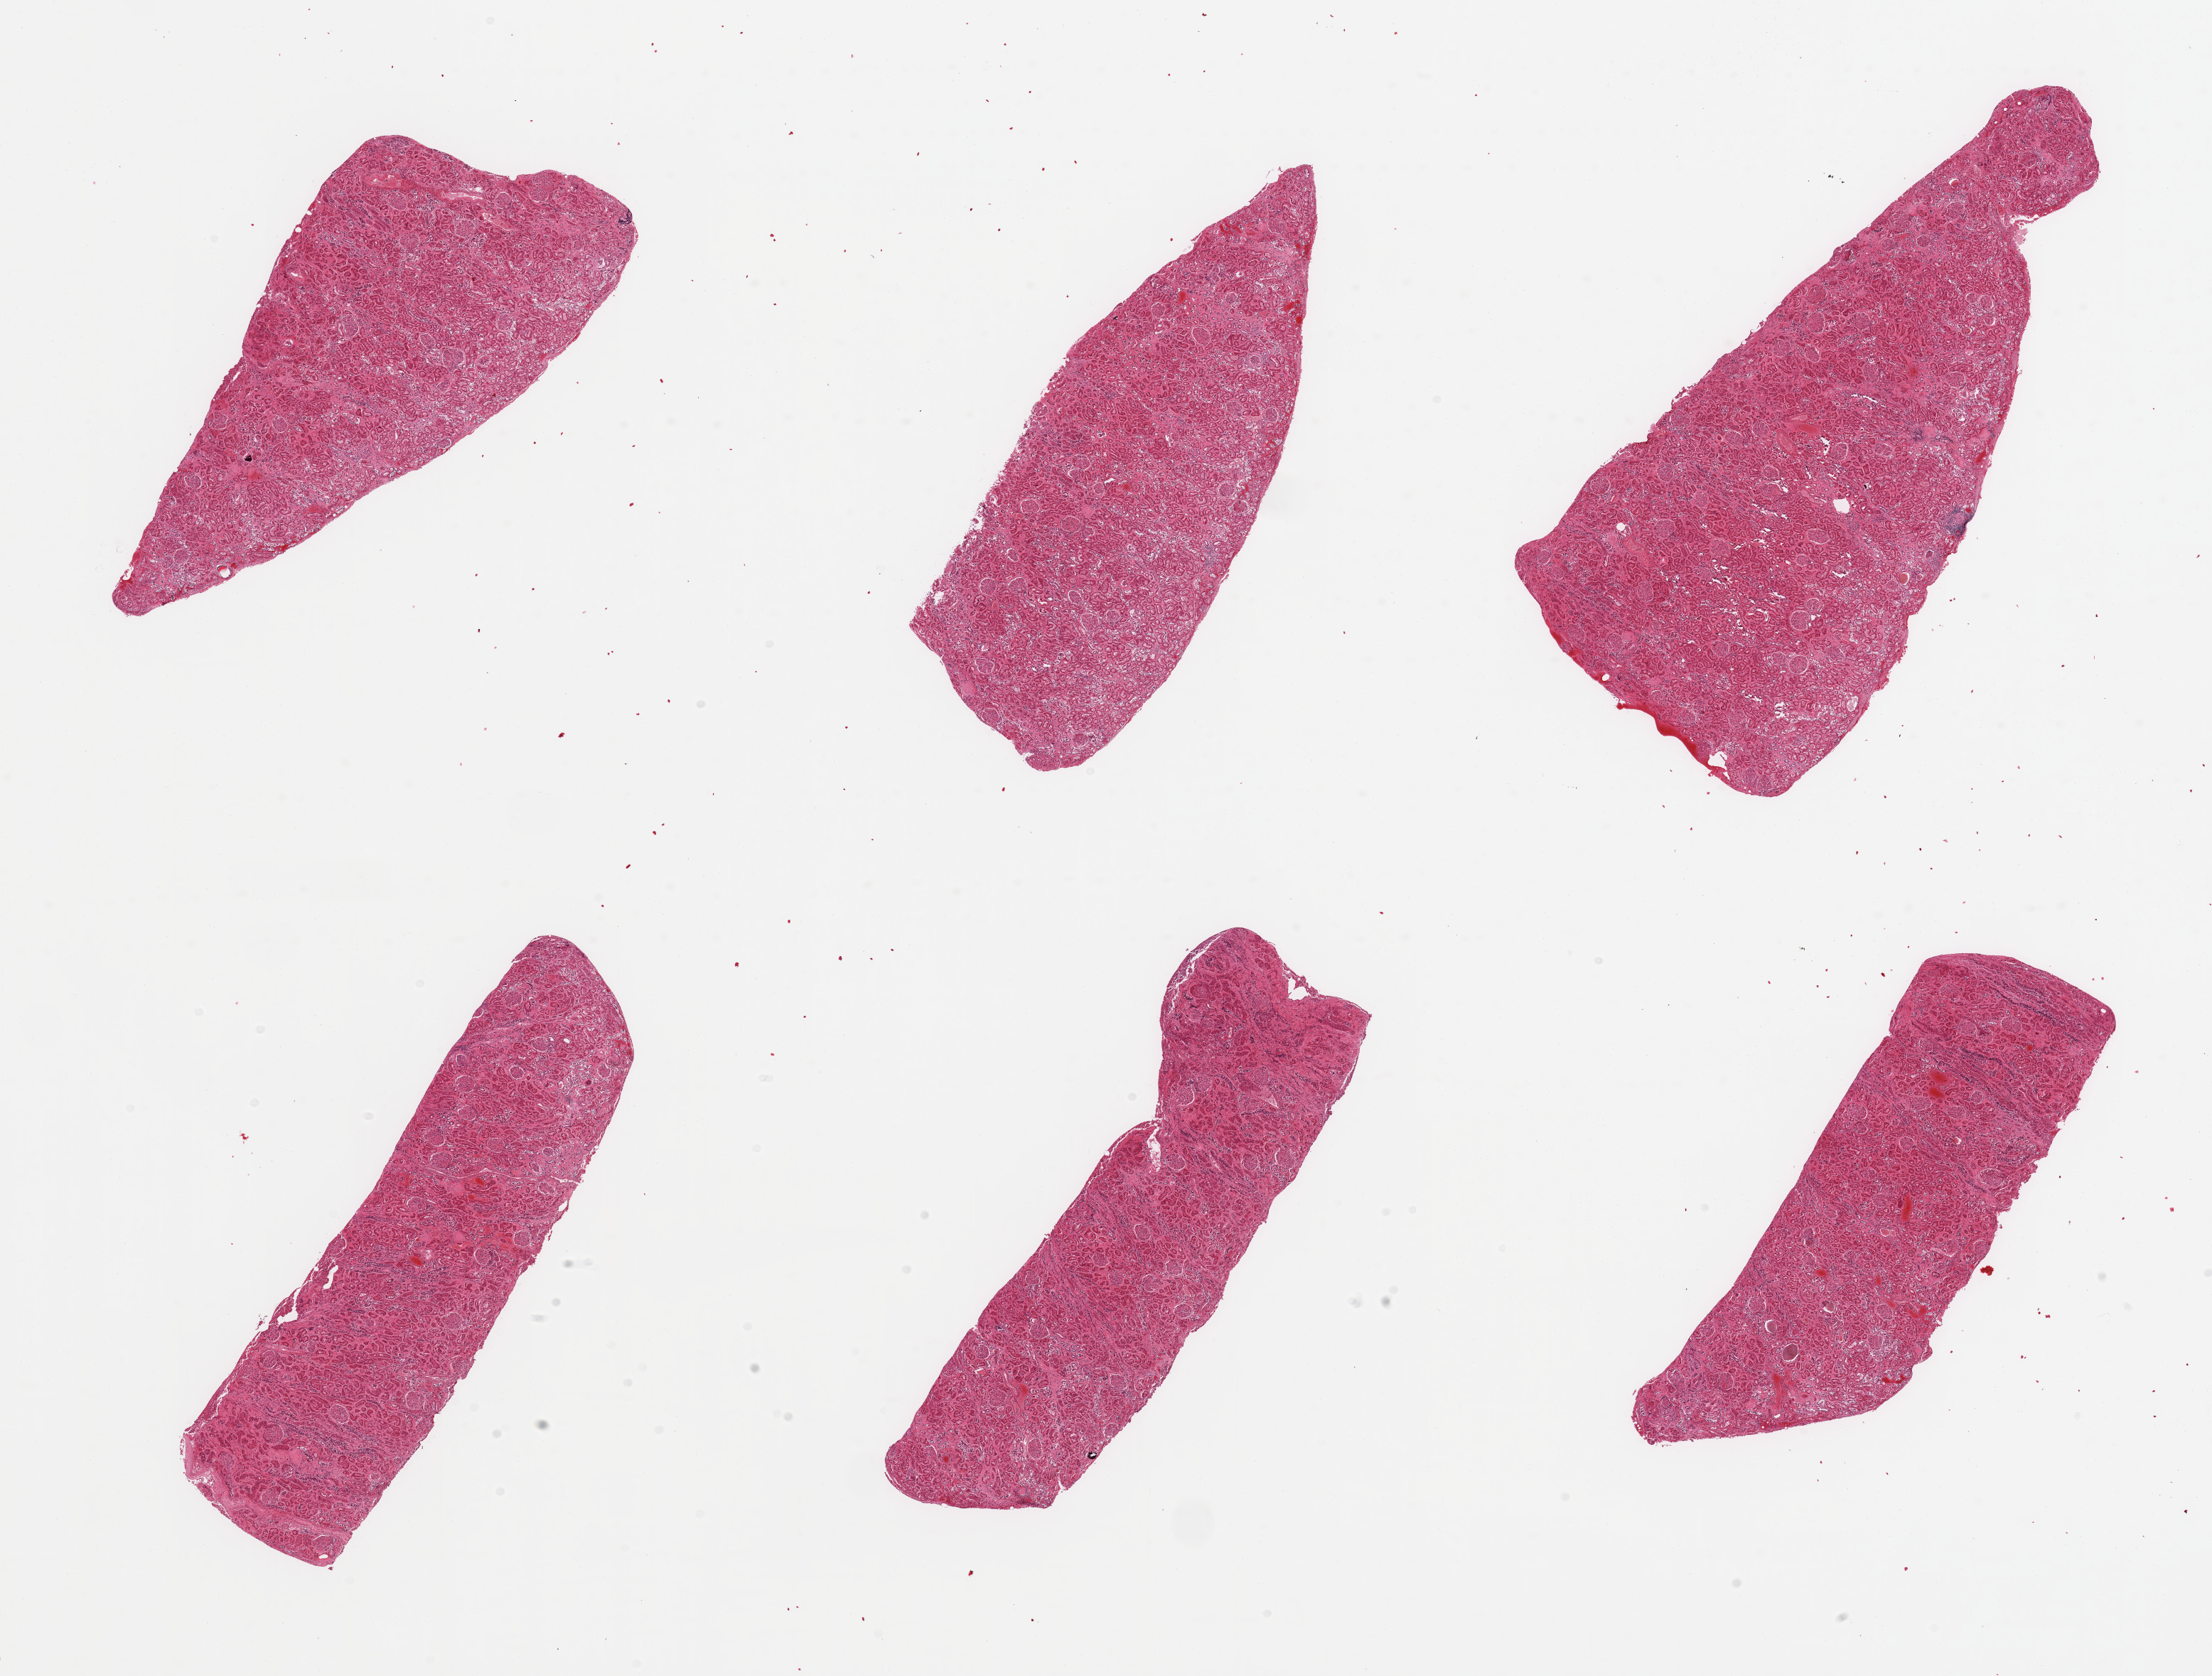
Whole-slide image, haematoxylin and eosin stain — shown as a low-resolution overview of the whole scanned area (about 24.6 x 18.6 mm, slide scanned at 20x). PAXgene-fixed, paraffin-embedded tissue. Sampled site (target tissue): renal cortex. Donor tissue sample.
Reviewer comment on this tissue sample: 6 pieces; glomeruli in all sections, few sclerotic.